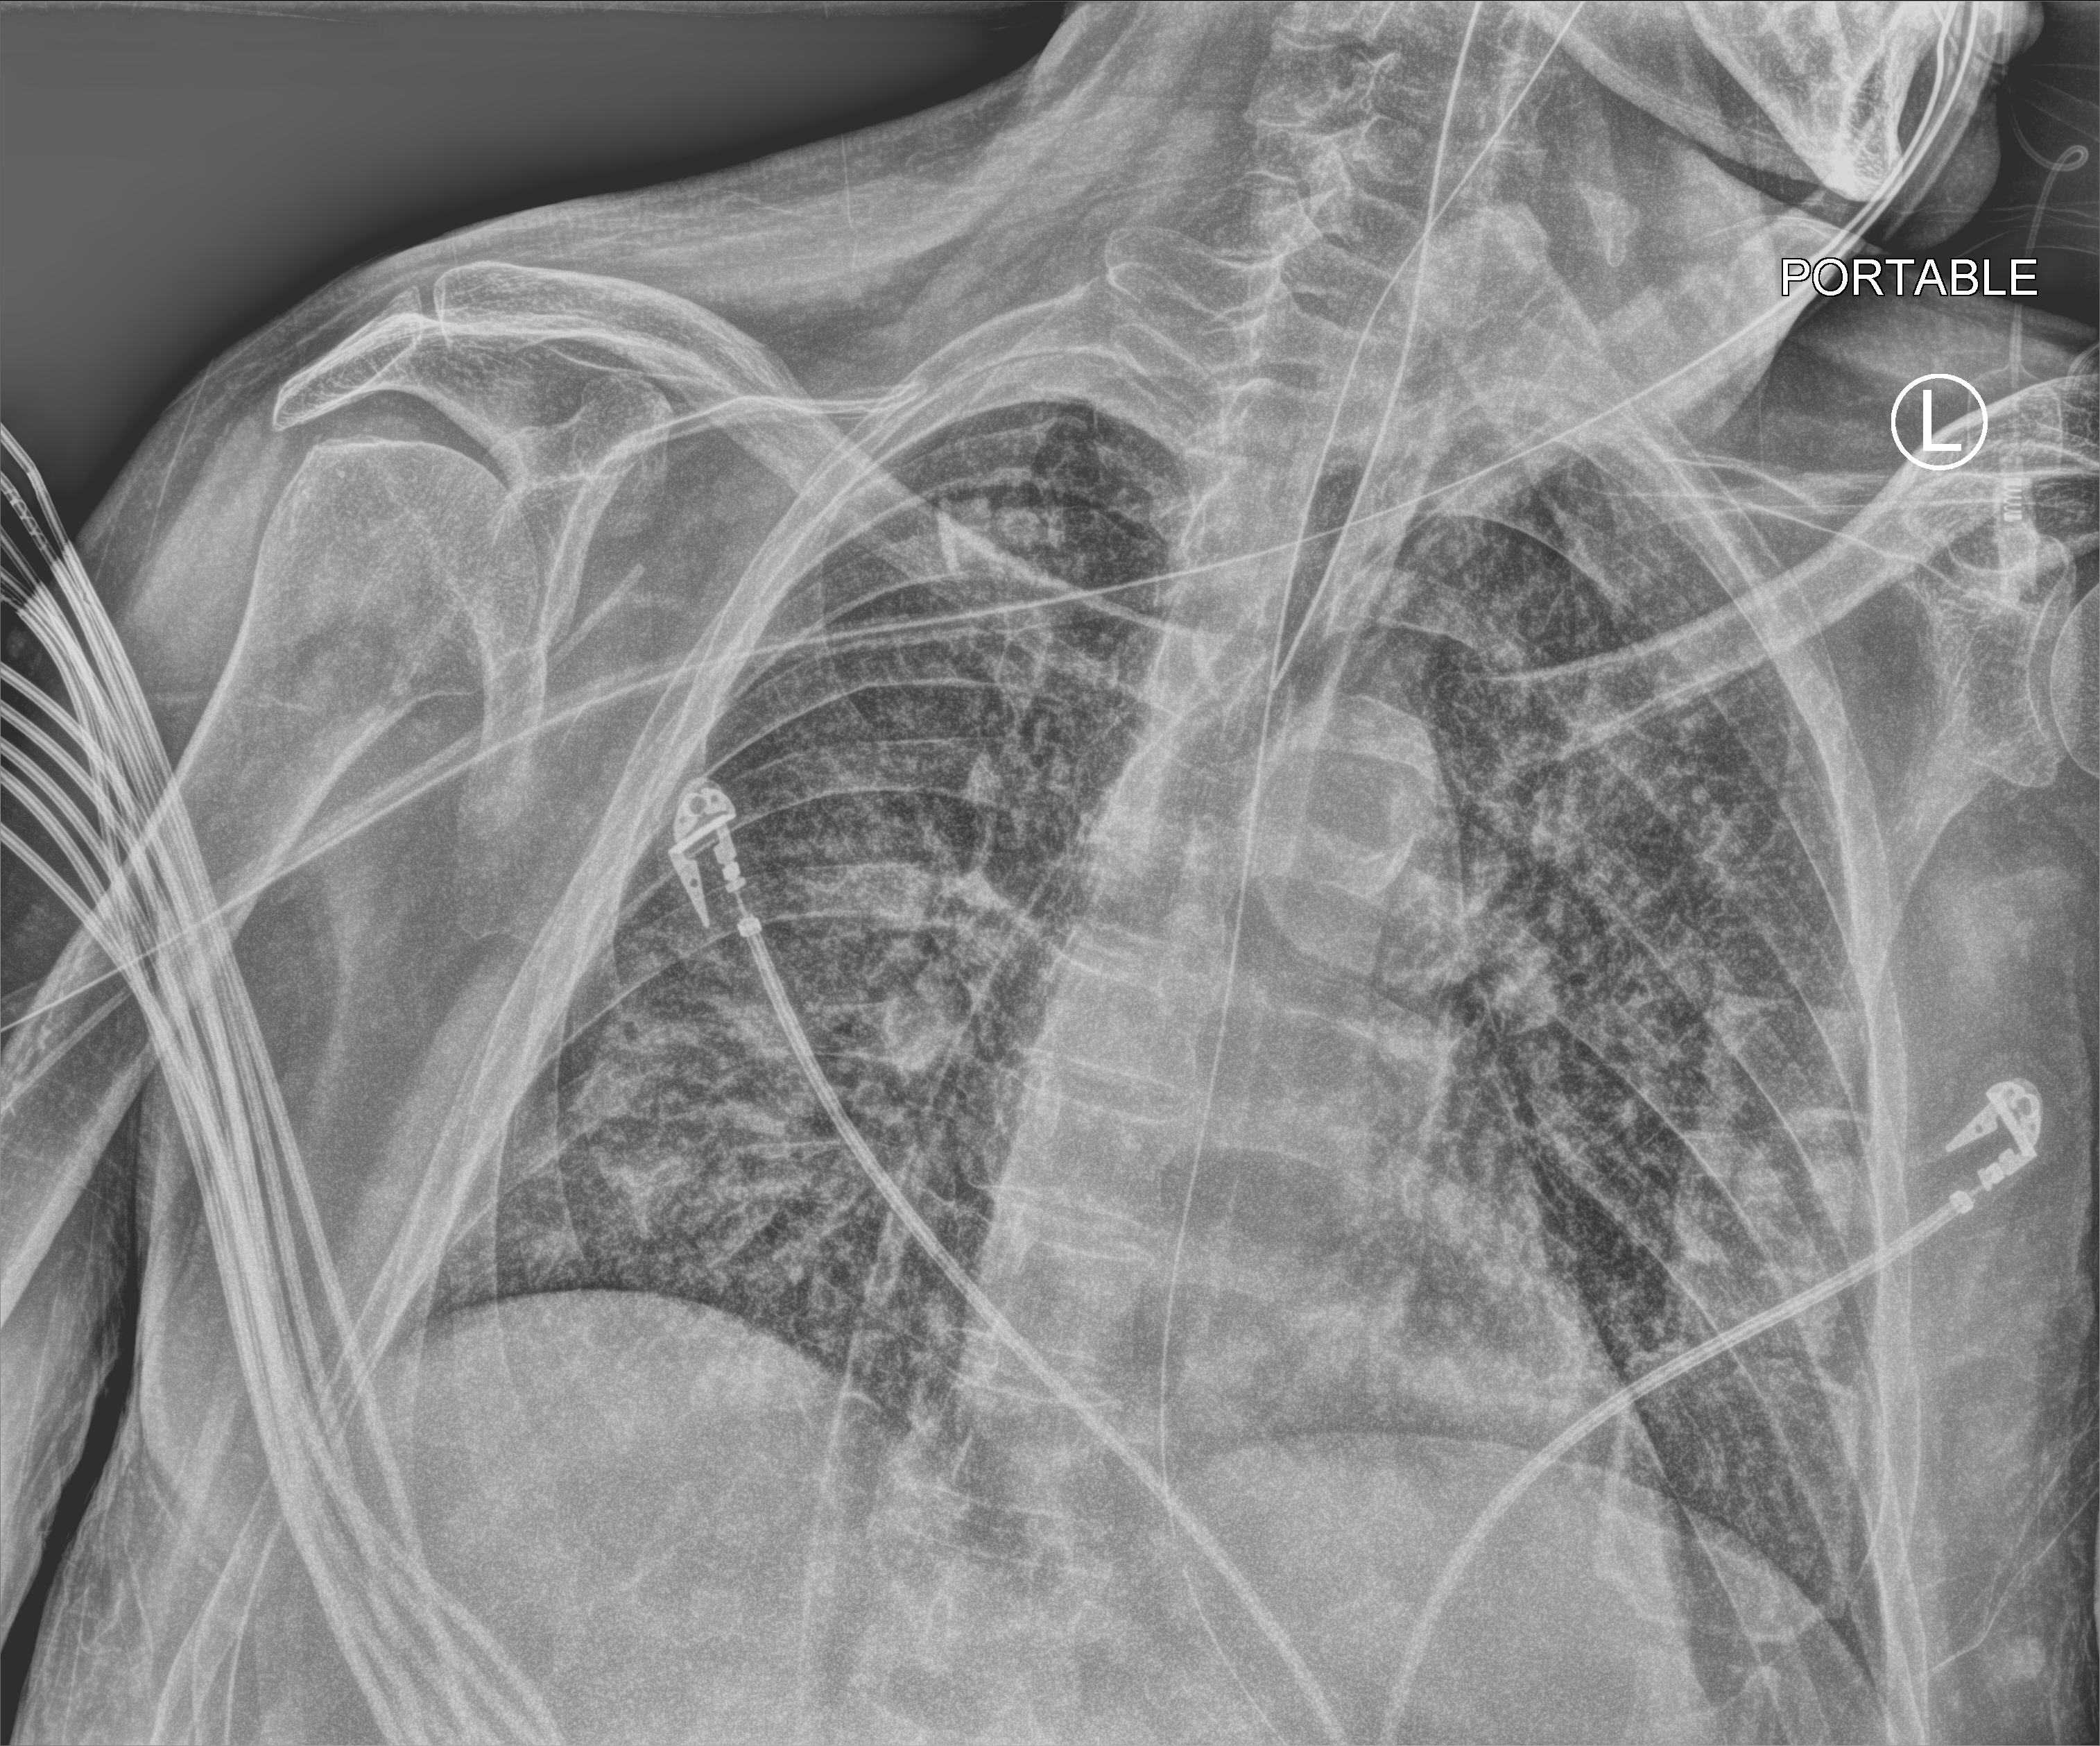
Bedside chest radiograph (computed radiography); anteroposterior (AP) projection. Patient hospitalised with COVID-19; male, aged 60–74 years.
Admission-level facts for this patient (not findings on this image; timing relative to this image not recorded): length of hospital stay: 25 days; admitted to intensive care during this hospital stay: yes.